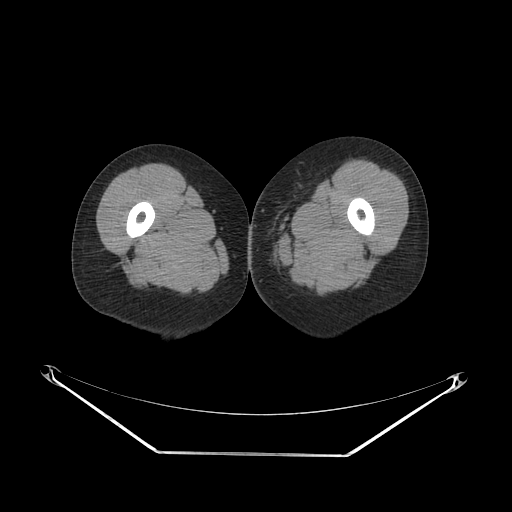
CT of an extremity soft-tissue mass (from a PET/CT study), one axial slice. Slice 34 of 267 in the series (ordered by position). Soft-tissue window (W 400 / L 40 HU). 3.75 mm slice thickness. 512 × 512 image matrix, field of view 500 × 500 mm. Female patient. From the clinical record (not read from this slice): histological type: leiomyosarcoma; grade: high; site of the primary tumour: groin.
Structures marked on this image (expert contour drawn on MRI and transferred to this co-registered scan by the dataset authors):
- gross tumour volume including surrounding oedema: bounding box [x1, y1, x2, y2] px = [249, 225, 277, 247]